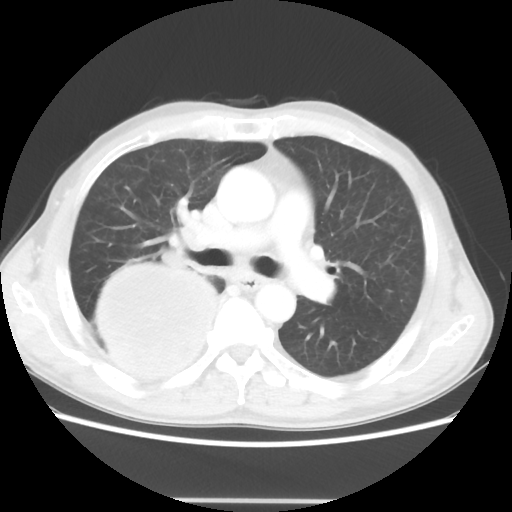
Chest CT, one axial slice; position 29 of 48 along the scan axis; reconstruction kernel STANDARD; 100 kVp; lung window (W 1500 / L -600 HU); 5 mm slice thickness; 512 × 512 image matrix, field of view 361 × 361 mm. Male patient, age 66 years. Case-level facts recorded for this patient, not image findings: clinical TNM (as recorded): T4 N1 M1.
Structures marked on this image (rectangle marked by the reading radiologist):
- lung tumour (recorded histology: small cell carcinoma): bounding box [x1, y1, x2, y2] px = [89, 254, 222, 381]